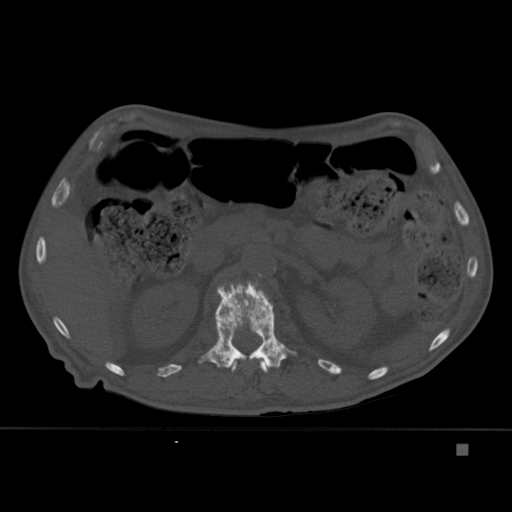
CT including the spine, one axial slice. Position 184 of 451 along the scan axis. Bone window (W 1800 / L 400 HU). 512 × 512 image matrix, field of view 378 × 378 mm. Male patient, age 75 years. Case-level facts recorded for this patient, not image findings: primary cancer: prostate.
Outlined on this slice (semi-automatically segmented with operator editing):
- L1 vertebra: box from (x=198, y=281) to (x=297, y=369) px
- T12 vertebra: (x=232, y=361)–(x=268, y=373)